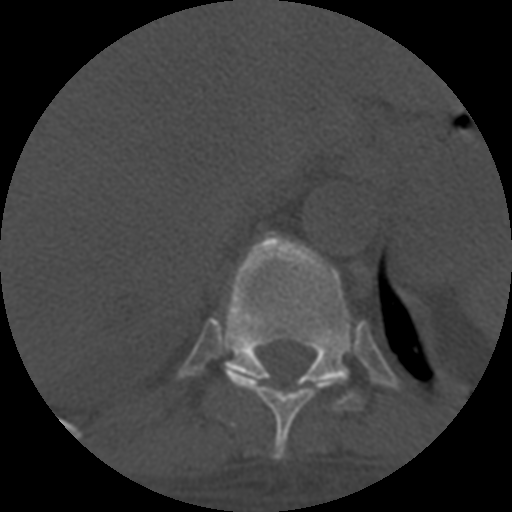
CT including the spine, one axial slice. Position 346 of 708 along the scan axis. Reconstruction kernel STANDARD. 120 kVp. One of 3 acquisitions stored at this slice position. Bone window (W 1800 / L 400 HU). 1.25 mm slice thickness. 512 × 512 image matrix, field of view 160 × 160 mm. Patient age 55 years. From the clinical record (not read from this slice): primary cancer: colon; vertebrae with lytic lesions (as recorded): T12, L1, L5.
Outlined on this slice (semi-automatically segmented with operator editing):
- T10 vertebra: bounding box [x1, y1, x2, y2] px = [225, 370, 332, 460]
- T11 vertebra: [224, 231, 367, 412]